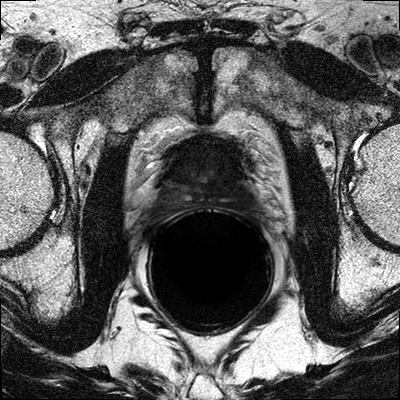
Multiparametric prostate MRI examination; 3 images, each a single mid-volume slice chosen by position (not for content). Treatment context recorded for this patient: No surgery, patient received radiation theraphy after ADT.
Image 1: T2-weighted axial slice, series "T2W_TSE_AX", slice 14 of 26.
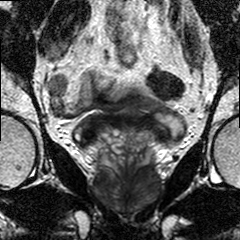
Image 2: T2-weighted coronal slice, series "T2W_TSE_COR", slice 13 of 24.
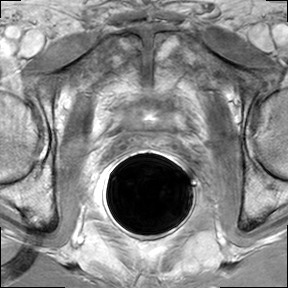
Image 3: axial dynamic contrast-enhanced (DCE) T1-weighted image, series "AX BLISS_GAD_8", slice 17 of 32, dynamic phase 5 of 8.
MRI report (verbatim):
FINDINGS: The prostate has a maximal lateral diameter of 4.5 cm, a maximal craniocaudal diameter of 3.1 cm and a maximal AP diameter of 2.6 cm resulting in an estimated gland volume of 20 cc. The zonal anatomy is not clearly preserved.
The entire prostate including central gland and bilateral peripheral zones show on the T2 weighted images diffuse hypo-intense signal alterations. There is also diffuse suspicious enhancement seen, involving diffusely the entire gland. At the left recto-prostatic angle, just below the seminal vesicals, the prostate border appears irregular and spiculated. (Slight location 33 series 401). This irregular border is seen only in the upper third (base) and is adjacent to the left neurovascular bundle. No evidence for seminal vesicles infiltration. No evidence of involvement of bladder neck and rectal wall. No suspiciously enlarged obturator or iliac lymph nodes. The osseous structures of the pelvic ring show diffuse geographic T2 and T1 weighted signal alteration with foci of atypical enhancement. Multiplanar reconstructions, subtraction images, and CAD analysis of the dynamic series for assessment of the kinetic information facilitated the interpretation of the exam.
IMPRESSION: 1) MRI findings suggestive for bilateral prostate cancer with diffuse involvement of the entire gland. The (Findings could be altered by prior therapy (status post radiation therapy?) and or diffuse high grade PIN mixed with cancerous tissue.) Beginning extracapsular extension at the left base posterior lateral likely. 2) Diffuse geographic MR-signal alterations of the osseous structures of the pelvic ring. Further assessment with bone scan/SPECT/PET/CT needed to assess for metastatic disease. 3) No evidence of seminal vesicles infiltration.

Prostate biopsy pathology (as recorded):
PROSTATE BIOPSIES A. LEFT BASE: PROSTATIC ADENOCARCINOMA, GLEASON SCORE 3+4=7/10, INVOLVING ABOUT 60% OF THE TISSUE SUBMITTED. PERINEURAL INVASION IS PRESENT. HIGH-GRADE PROSTATIC INTRAEPITHELIAL NEOPLASIA (PIN) IS PRESENT. B. LEFT LATERAL BASE: PROSTATIC ADENOCARCINOMA, GLEASON SCORE 3+4=7/10, INVOLVING ABOUT 90% OF THE TISSUE SUBMITTED. PERINEURAL INVASION IS PRESENT. C. LEFT MID: PROSTATIC ADENOCARCINOMA, GLEASON SCORE 3+4=7/10, INVOLVING ABOUT 75% OF THE TISSUE SUBMITTED. PERINEURAL INVASION IS PRESENT. D. LEFT LATERAL MID: PROSTATIC ADENOCARCINOMA, GLEASON SCORE 3+4=7/10, INVOLVING ABOUT 80% OF THE TISSUE SUBMITTED. E. LEFT APEX: PROSTATIC ADENOCARCINOMA, GLEASON SCORE 3+4=7/10, INVOLVING ABOUT 70% OF THE TISSUE SUBMITTED. F. LEFT LATERAL APEX: PROSTATIC ADENOCARCINOMA, GLEASON SCORE 3+3=6/10, INVOLVING ABOUT 60% OF THE TISSUE SUBMITTED. G. RIGHT BASE: PROSTATIC ADENOCARCINOMA, GLEASON SCORE 3+4=7/10, INVOLVING ABOUT 75% OF THE TISSUE SUBMITTED. H. RIGHT LATERAL BASE: PROSTATIC ADENOCARCINOMA, GLEASON SCORE 3+4=7/10, INVOLVING ABOUT 80% OF THE TISSUE SUBMITTED. I. RIGHT MID: PROSTATIC ADENOCARCINOMA, GLEASON SCORE 3+3=6/10, INVOLVING ABOUT 60% OF THE TISSUE SUBMITTED. HIGH-GRADE PROSTATIC INTRAEPITHELIAL NEOPLASIA (PIN) IS PRESENT. J. RIGHT LATERAL MID: PROSTATIC ADENOCARCINOMA, GLEASON SCORE 3+4=7/10, INVOLVING ABOUT 80% OF THE TISSUE SUBMITTED. HIGH-GRADE PROSTATIC INTRAEPITHELIAL NEOPLASIA (PIN) IS PRESENT. K. RIGHT APEX: PROSTATIC ADENOCARCINOMA, GLEASON SCORE 3+4=7/10, INVOLVING ABOUT 70% OF THE TISSUE SUBMITTED. HIGH-GRADE PROSTATIC INTRAEPITHELIAL NEOPLASIA (PIN) IS PRESENT. L. RIGHT LATERAL APEX: BLOOD CLOT ONLY, INSUFFICIENT TISSUE FOR DIAGNOSIS